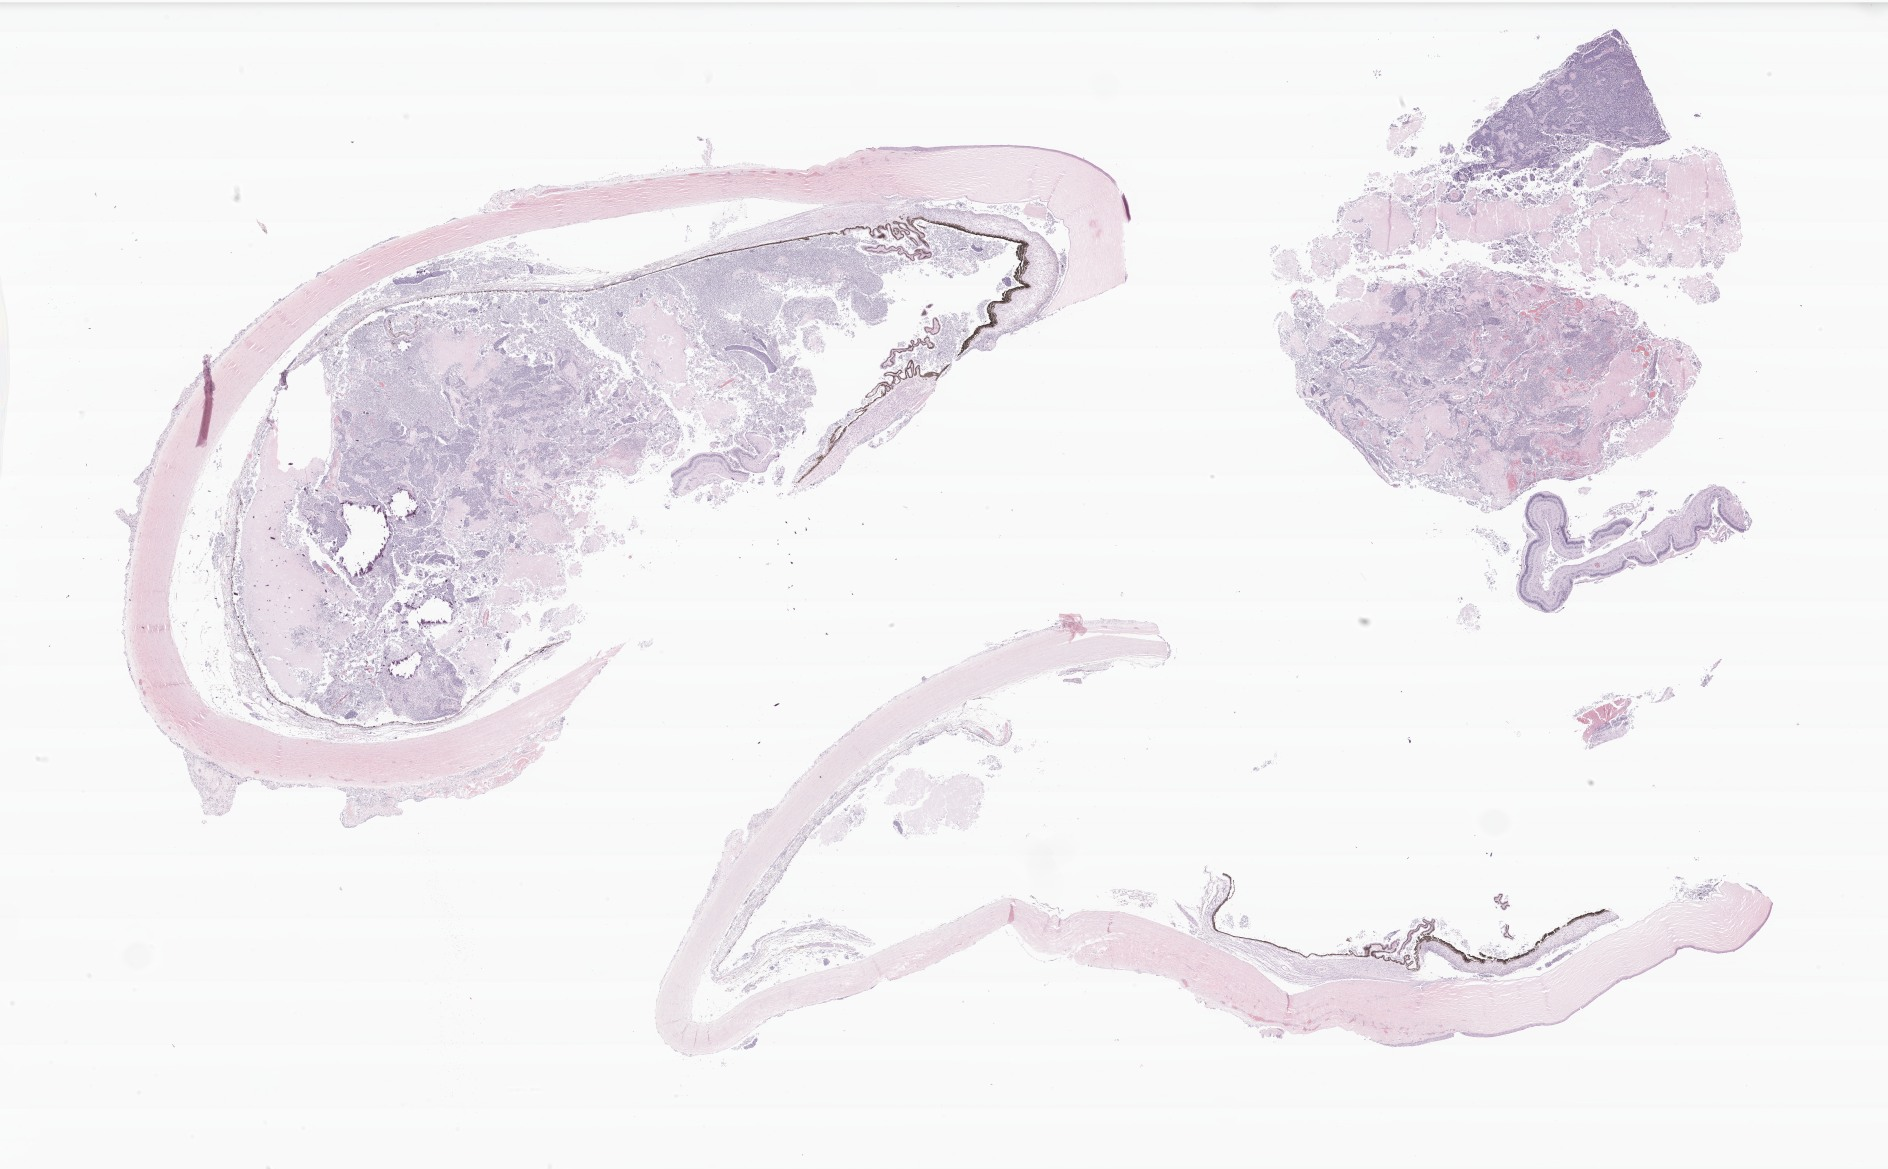
Whole-slide image, H&E stain of tumor tissue from the retina — a low-resolution overview of the entire scanned area, about 31.8 x 19.7 mm. Formalin-fixed, paraffin-embedded (FFPE) tissue. Patient male; age 38 months (3 years 2 months).
Recorded diagnosis: Retinoblastoma, NOS.